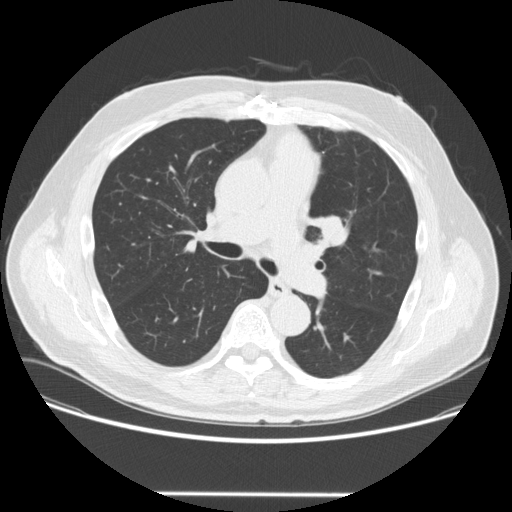
Axial slice from a low-dose chest CT screening exam, third screening round (two years after baseline), lung window (W 1500 / L -600 HU), 2.5 mm slice thickness. Male participant, aged 66 years at enrolment. Former smoker at enrolment.
• Lesion marked by an expert reader, box from (x=306, y=206) to (x=358, y=254) px.
• The screening reader recorded 2 non-calcified nodules or masses ≥4 mm on this exam (left upper lobe, right lower lobe); which of them this box marks is not recorded.
• Official screen result: positive, other.